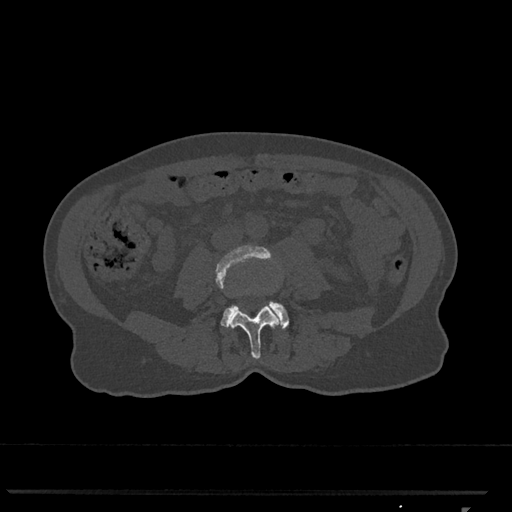
CT including the spine, one axial slice. Slice 246 of 793 in the series (ordered by position). 120 kVp. Bone window (W 1800 / L 400 HU). 0.5 mm slice thickness. 512 × 512 image matrix, field of view 380 × 380 mm. Patient: female, 62 years. From the clinical record (not read from this slice): primary cancer: renal.
Outlined on this slice (semi-automatic segmentation, software-assisted and operator-edited):
- L3 vertebra: box from (x=215, y=245) to (x=283, y=359) px
- L4 vertebra: (x=221, y=301)–(x=289, y=330)